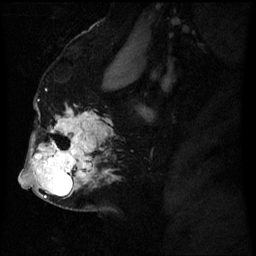
Breast MRI (dynamic contrast-enhanced), one sagittal slice. Position 38 of 60 along the scan axis. Dynamic contrast-enhanced series, image 2 of 3 at this slice position (ordered by acquisition). 1.5 T. TE 4.2 ms, TR 8 ms. 2.5 mm slice thickness. 256 × 256 image matrix, field of view 200 × 200 mm. Patient: female, 50 years.
Annotated regions visible in this slice (semi-automatically segmented with operator editing):
- analysis volume of interest (the breast-tissue region the enhancement analysis was run in; not a lesion): bounding box [x1, y1, x2, y2] px = [24, 118, 105, 199]
- tumour enhancement mask (voxels above the 70 % enhancement threshold inside the analysis volume of interest): [33, 124, 87, 181]